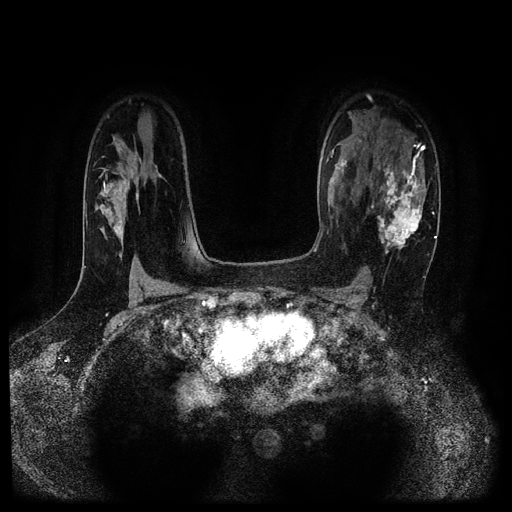
Breast MRI (dynamic contrast-enhanced, multi-phase), one axial slice. Slice 71 of 116 in the series (ordered by position). Dynamic contrast-enhanced series, time point 2 of 5 at this slice position (early post-contrast). 1.5 T. TE 2.7 ms, TR 5.4 ms. 512 × 512 image matrix. Female patient, age 43 years.
Outlined on this slice (semi-automatic segmentation, software-assisted and operator-edited):
- breast lesion (labelled 'tumour' in the annotation; benign lesions carry a separate 'benign' label): bounding box (x1, y1, x2, y2) in pixels: (377, 163, 426, 260)